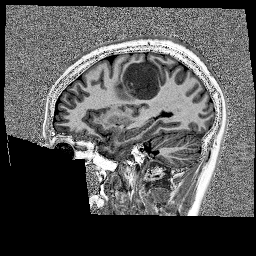
Brain MRI from a brain-tumour surgery series, one sagittal slice. 1 mm slice thickness. 256 × 256 image matrix, field of view 256 × 256 mm. From the clinical record (not read from this slice): histopathology: Glioblastoma; WHO grade: 4; IDH mutation: no.
Outlined on this slice (outlined manually by an expert reader):
- tumour: bounding box <136,58,174,105> (left, top, right, bottom; pixels)